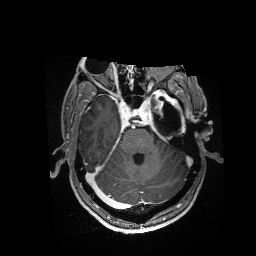
Brain MRI from a brain-tumour surgery series, one axial slice. T1-weighted post-contrast. 1 mm slice thickness. 256 × 256 image matrix, field of view 256 × 256 mm. From the clinical record (not read from this slice): histopathology: Glioblastoma; WHO grade: 4.
Structures marked on this image (expert manual segmentation):
- residual tumour: bounding box (x1, y1, x2, y2) in pixels: (154, 91, 182, 113)